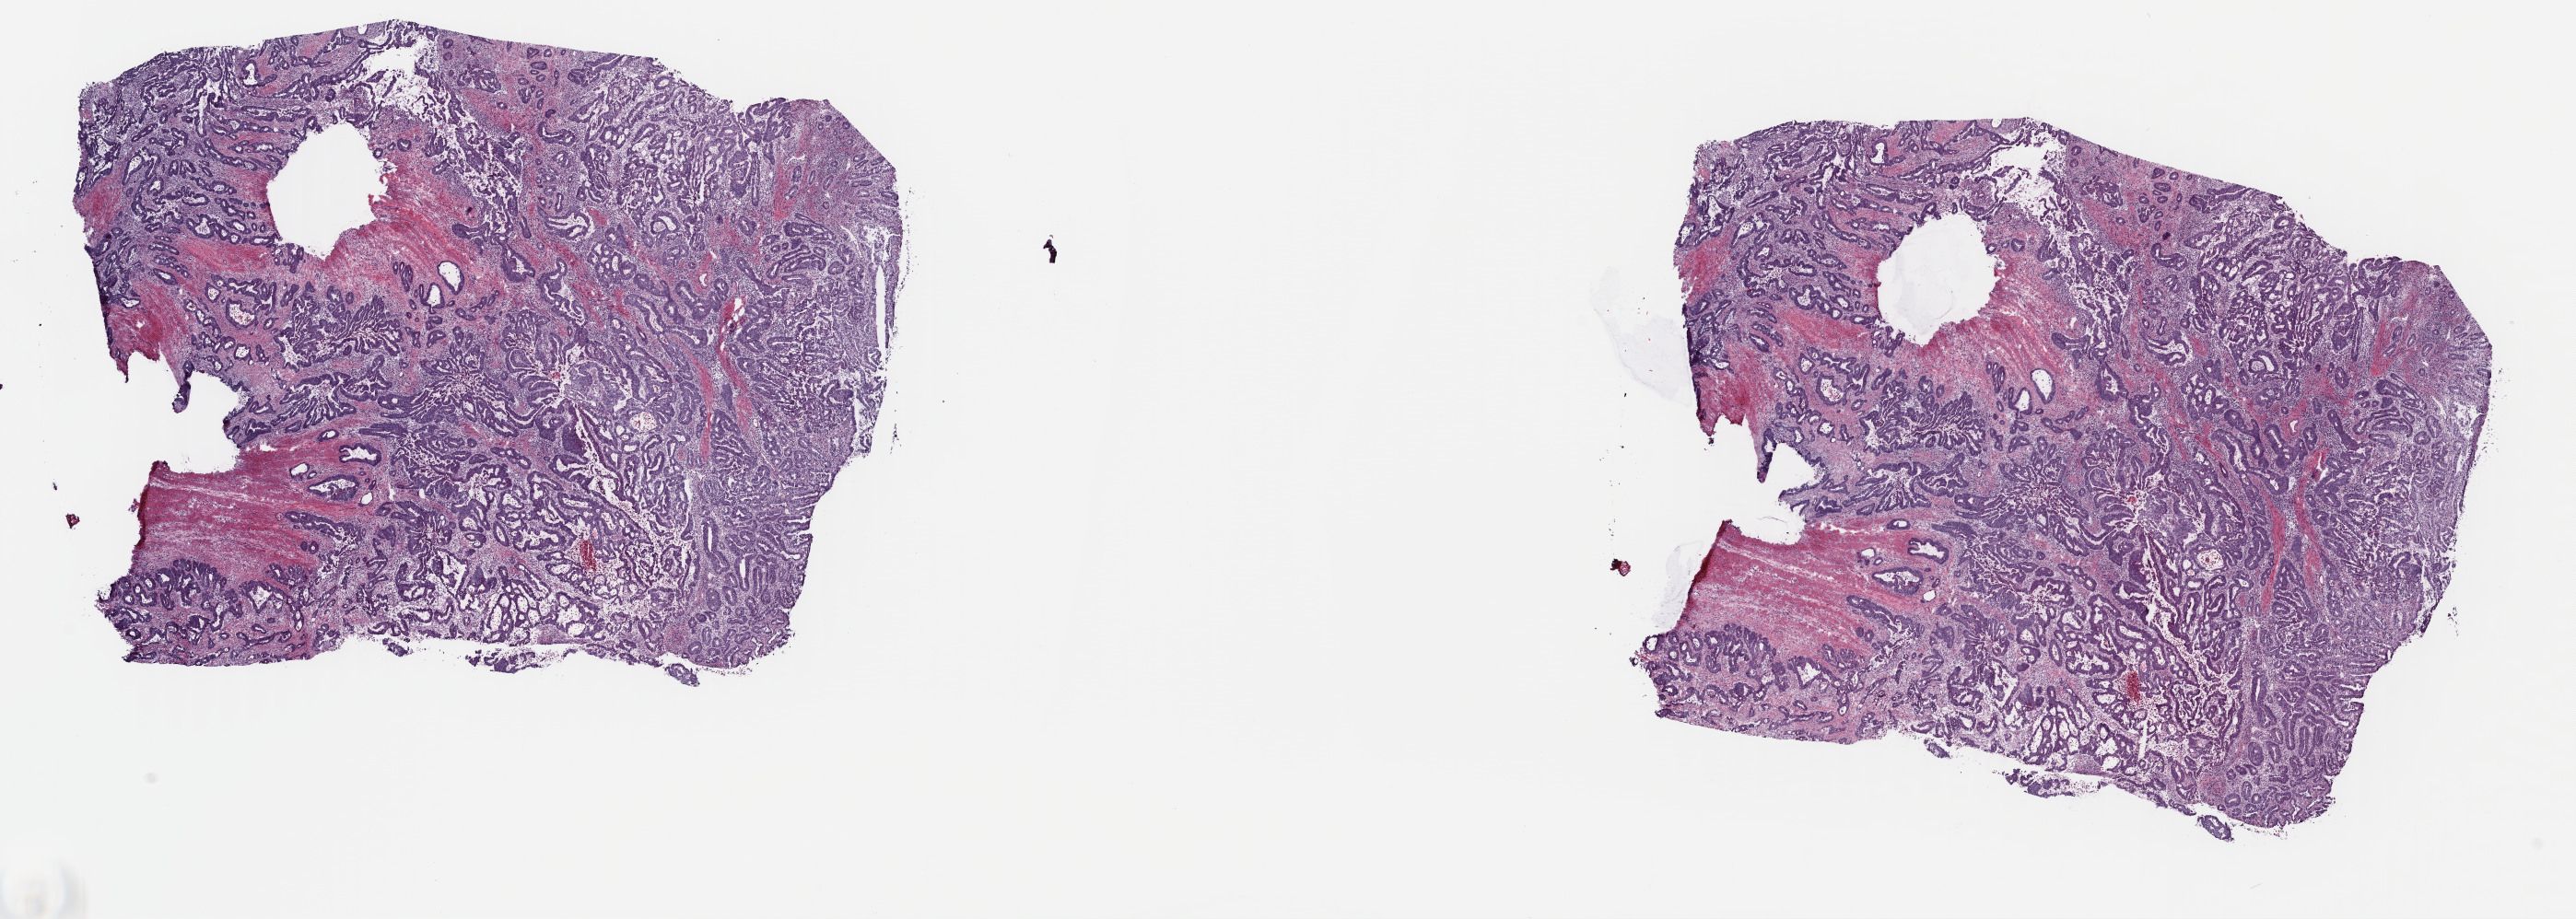
H&E whole-slide image — shown as a low-resolution overview of the whole scanned area (about 22.0 x 7.8 mm); frozen section from the top of the tissue portion; sample: primary tumour, colon. Male patient; age at initial diagnosis 71 years. Pathologist review of this section (percent, as recorded): tumour cells 99%, tumour nuclei 65%, normal cells 0%, stromal cells 0%, necrosis 1%. Infiltration values recorded for this section: lymphocyte infiltration 5%, monocyte infiltration 1%, neutrophil infiltration 1%.
- lymph nodes positive (case pathology): 3 of 38 examined
- diagnosis: Adenocarcinoma, NOS
- AJCC pathologic stage: IIIB (7th edition)